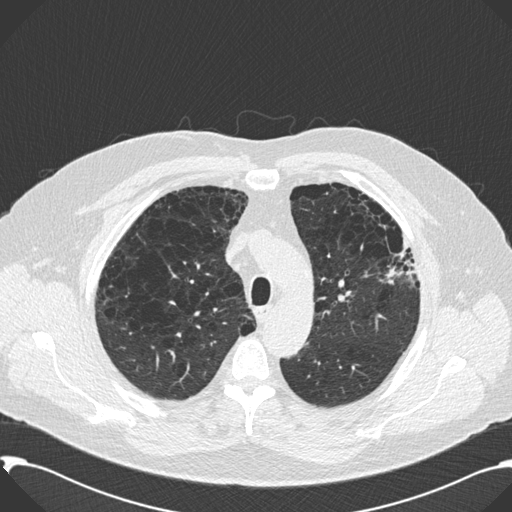
Chest CT (low-dose screening protocol), one axial image. Second screening round (one year after baseline). Lung window (W 1500 / L -600 HU). 2 mm slice thickness. 120 kVp. Slice 44 of 199 in the series. Male, age 59 years at enrolment.
Lesion marked by an expert reader, bounding box [x1, y1, x2, y2] px = [363, 215, 419, 297]. Screening reader's record for this exam: no non-calcified nodule ≥4 mm recorded. Official screen result: negative screen, significant abnormalities not suspicious for lung cancer. Lung cancer was diagnosed 518 days after this screen: bronchiolo-alveolar carcinoma, mixed mucinous and non-mucinous, left upper lobe, stage IA (AJCC 6th edition), 20 mm at pathology.